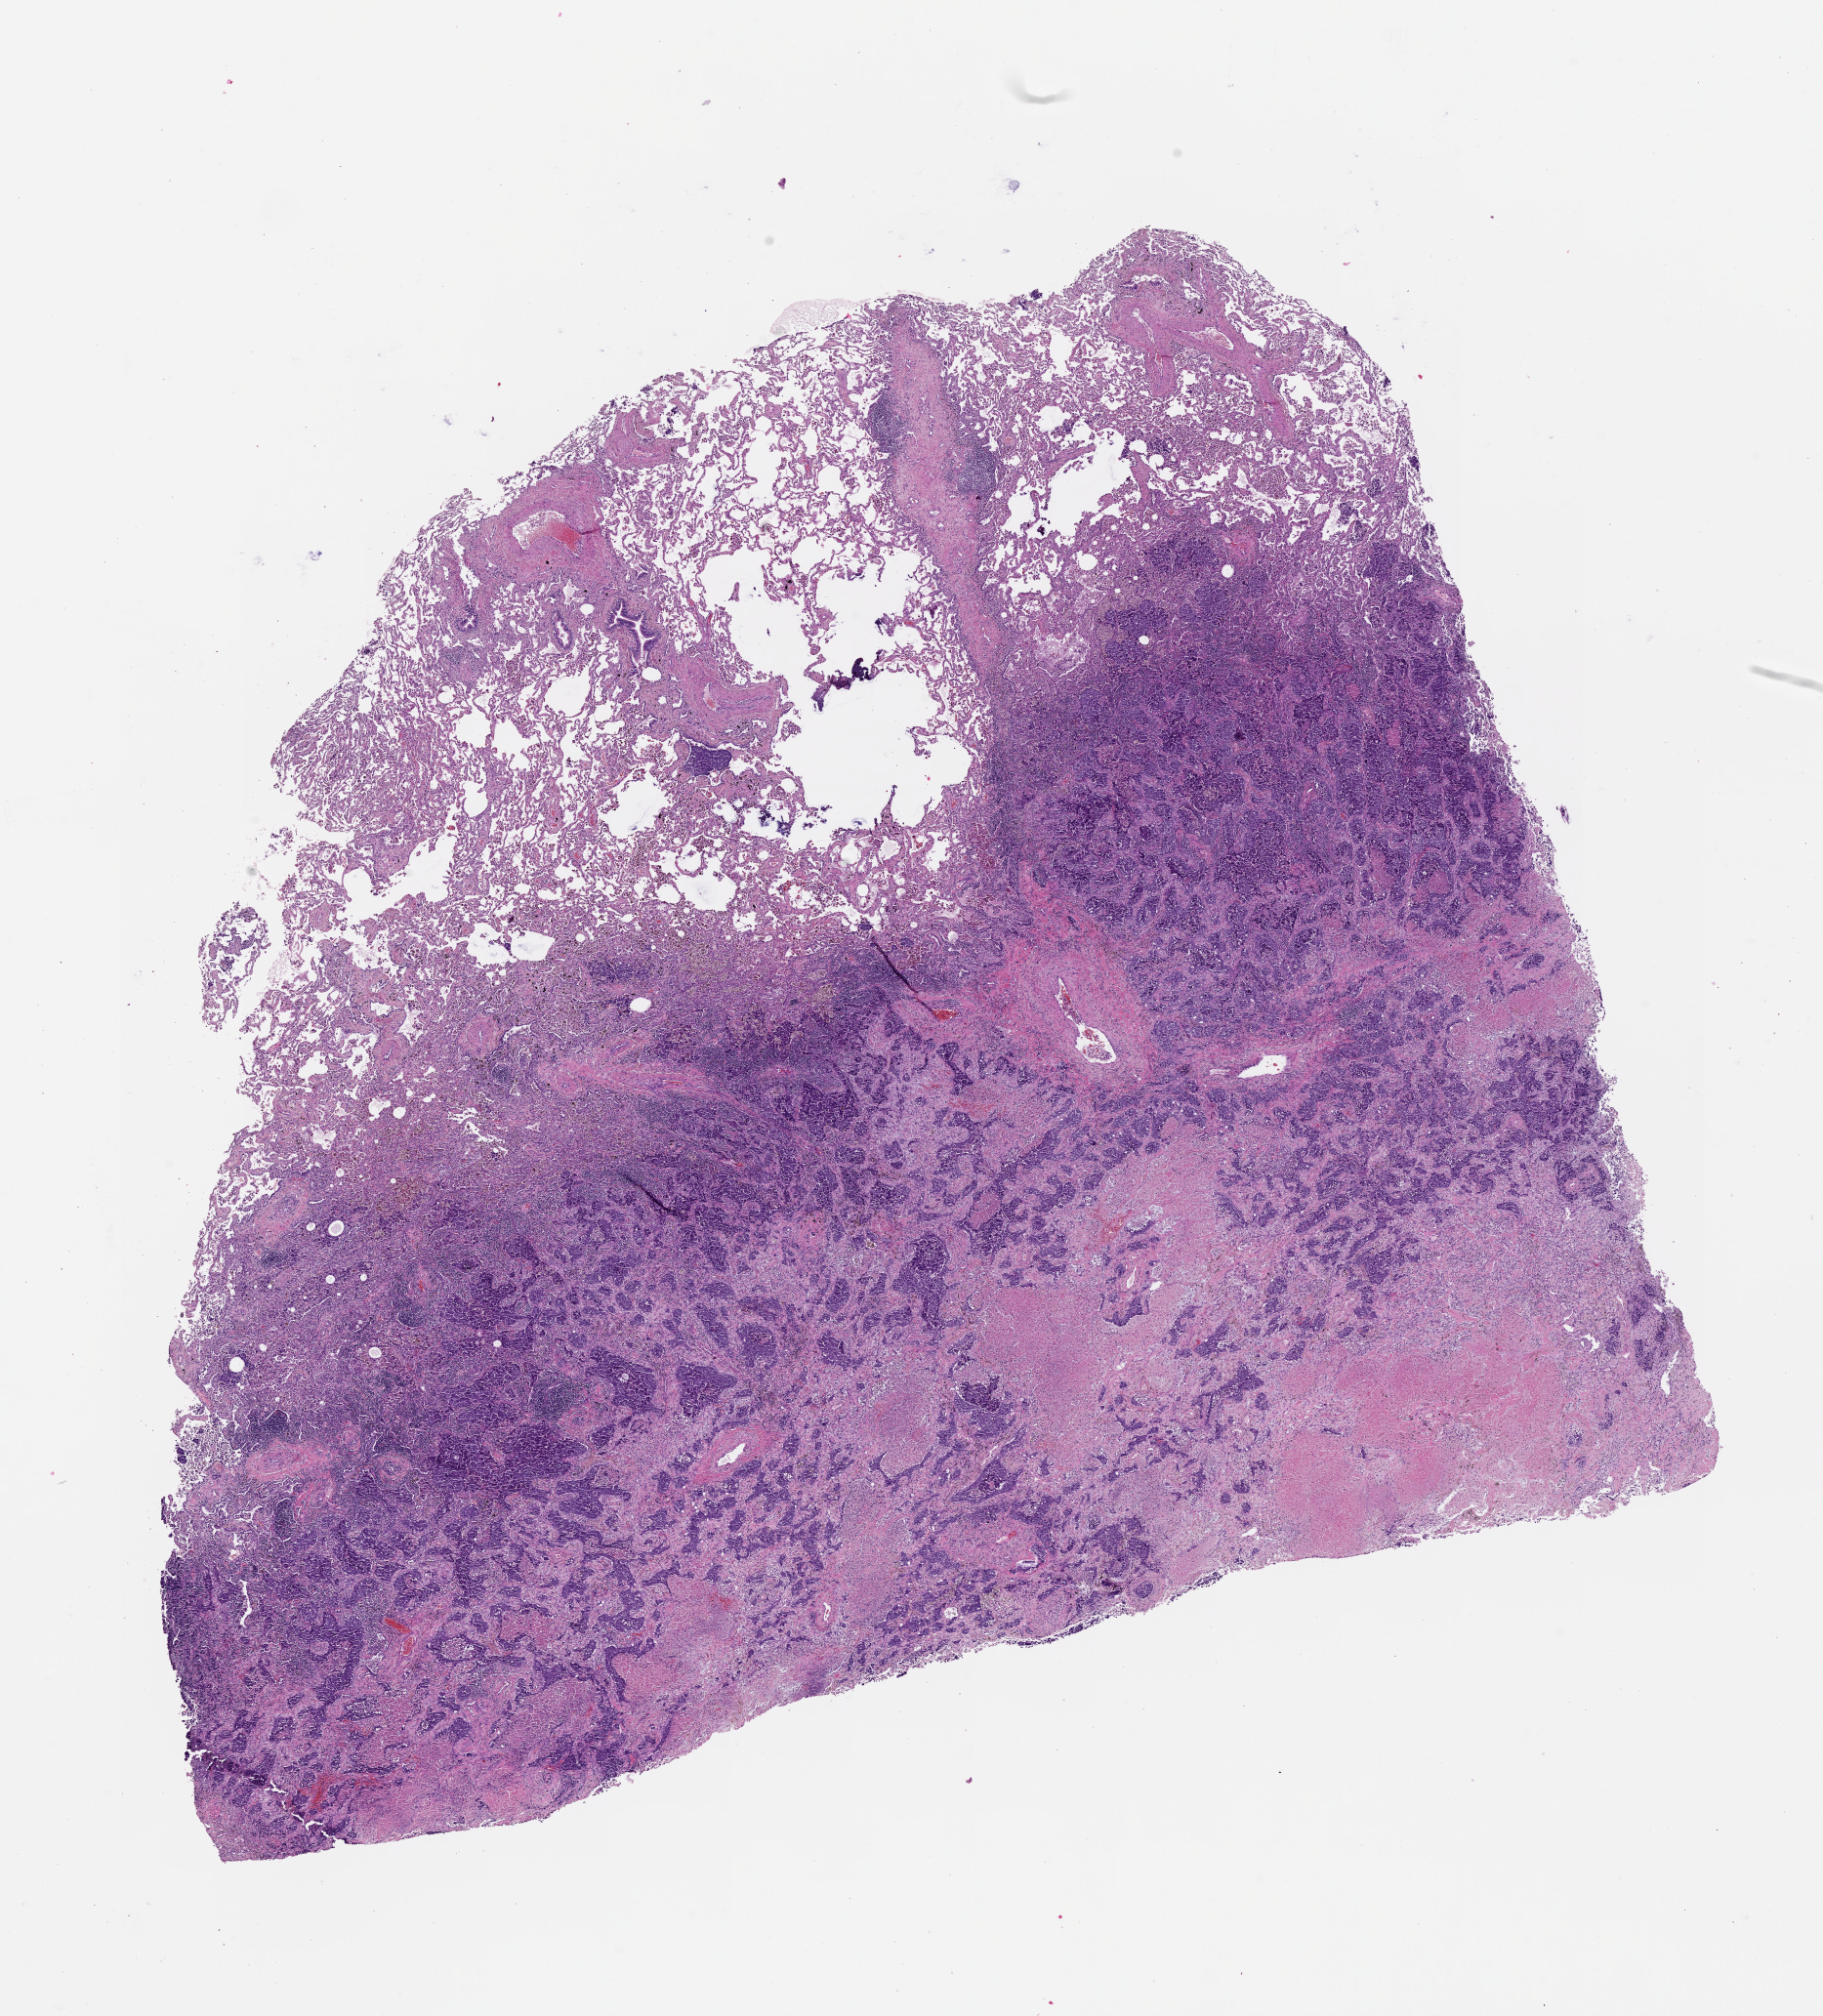
Whole-slide histology image, Hematoxylin and eosin (H&E) stained, a low-resolution overview of the entire scanned area, about 15.0 x 16.6 mm. Lung, tumour tissue. Male, 60 y/o.
Patient diagnosis (cohort enrolment): squamous cell carcinoma (lung).